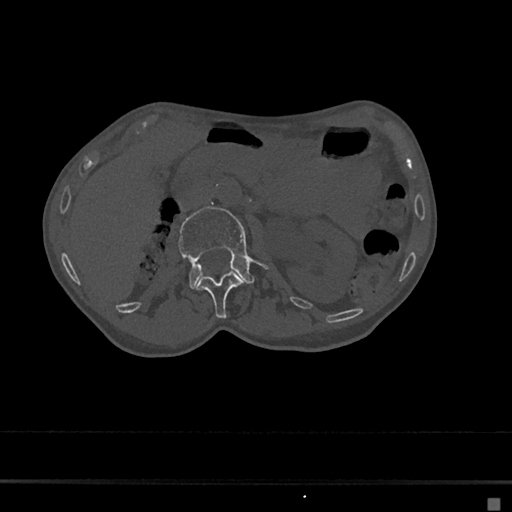
CT including the spine, one axial slice; reconstruction kernel Br40s/3; 120 kVp; bone window (W 1800 / L 400 HU); 0.5 mm slice thickness; 512 × 512 image matrix, field of view 360 × 360 mm. Female patient, age 68 years. From the clinical record (not read from this slice): primary cancer: renal.
Annotated regions visible in this slice (semi-automatic segmentation, software-assisted and operator-edited):
- L1 vertebra: bounding box (x1, y1, x2, y2) in pixels: (196, 266, 242, 319)
- L2 vertebra: (178, 206, 254, 288)